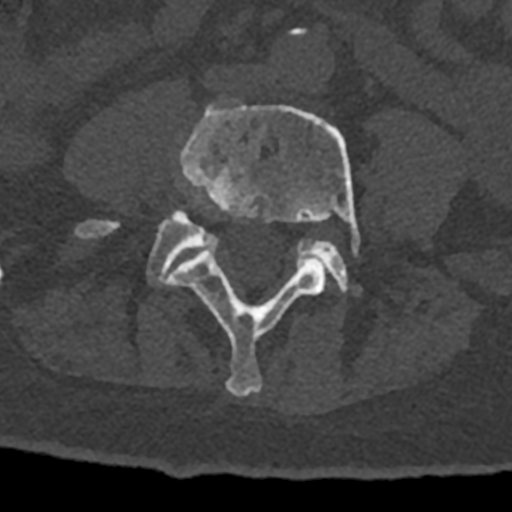
CT including the spine, one axial slice; position 240 of 797 along the scan axis; 120 kVp; bone window (W 1800 / L 400 HU); 0.5 mm slice thickness; 512 × 512 image matrix. Patient: male, 74 years. Case-level facts recorded for this patient, not image findings: primary cancer: renal.
Structures marked on this image (semi-automatically segmented with operator editing):
- L4 vertebra: box from (x=167, y=100) to (x=360, y=397) px
- L5 vertebra: (x=77, y=213)–(x=350, y=292)